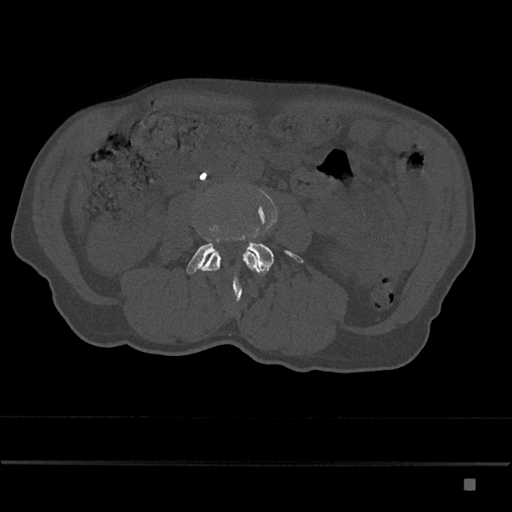
CT including the spine, one axial slice; position 370 of 797 along the scan axis; reconstruction kernel Br40s/3; 120 kVp; bone window (W 1800 / L 400 HU); 0.5 mm slice thickness; 512 × 512 image matrix, field of view 390 × 390 mm. Male patient, age 72 years. From the clinical record (not read from this slice): primary cancer: prostate.
Annotated regions visible in this slice (semi-automatic segmentation, software-assisted and operator-edited):
- L3 vertebra: bounding box <202,191,260,302> (left, top, right, bottom; pixels)
- L4 vertebra: <186,193,304,275>